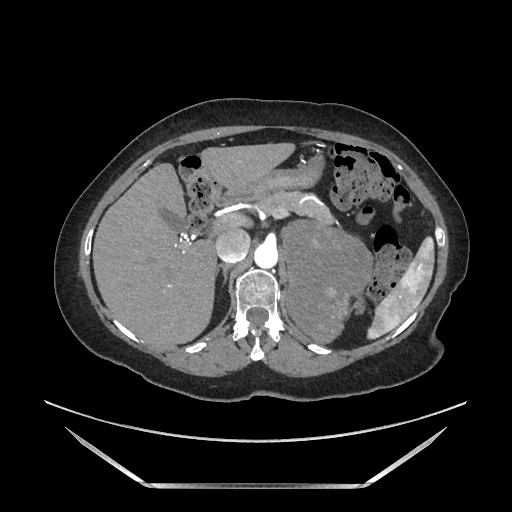
Contrast-enhanced abdominal CT, one axial slice. Slice 116 of 205 in the series (ordered by position). Soft-tissue window (W 400 / L 40 HU). 1.25 mm slice thickness. 512 × 512 image matrix, field of view 440 × 440 mm. Female patient. Case-level facts recorded for this patient, not image findings: diagnosis: adrenocortical carcinoma; tumour side: left adrenal; tumour size at pathology: 12.5 cm; Ki-67 index: 39 %; stage (as recorded): 3.
Structures marked on this image (semi-automatically segmented with operator editing):
- mass: bounding box (x1, y1, x2, y2) in pixels: (288, 223, 372, 337)